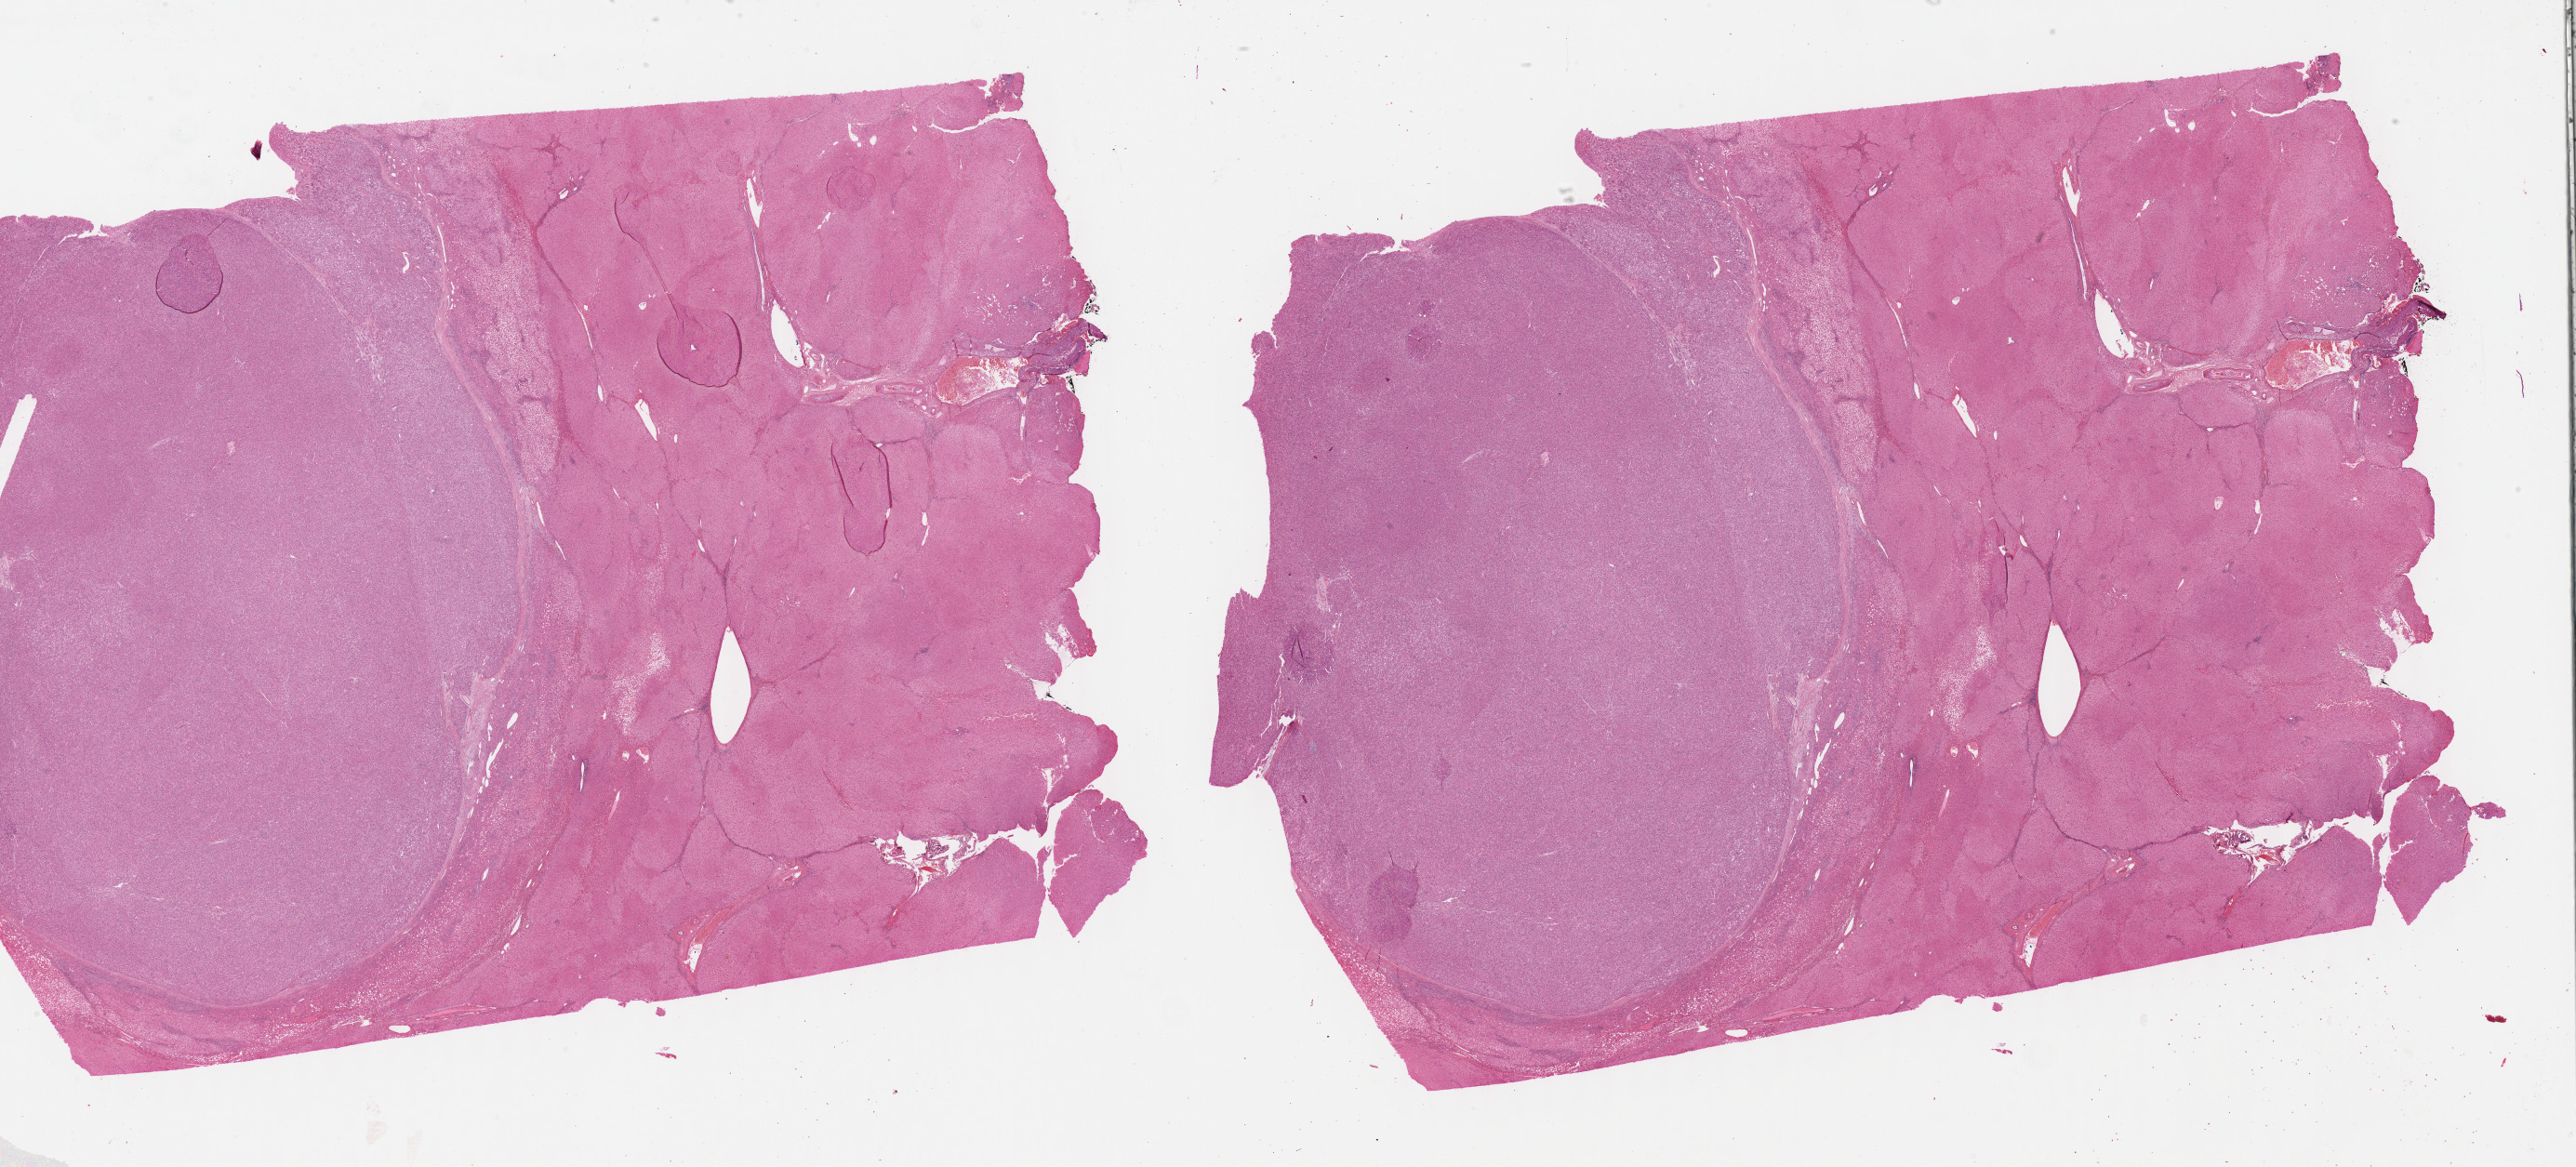
H&E-stained whole-slide image, shown as a low-resolution overview of the whole scanned area (about 44.8 x 20.3 mm, slide scanned at 40x), FFPE section, primary tumour sample from the liver. Female patient; age at initial diagnosis 43 years. Histologic grade: G2 (moderately differentiated).
AJCC pathologic stage: I (7th edition). TNM: T1 NX MX. Histologic diagnosis: Hepatocellular carcinoma, NOS.